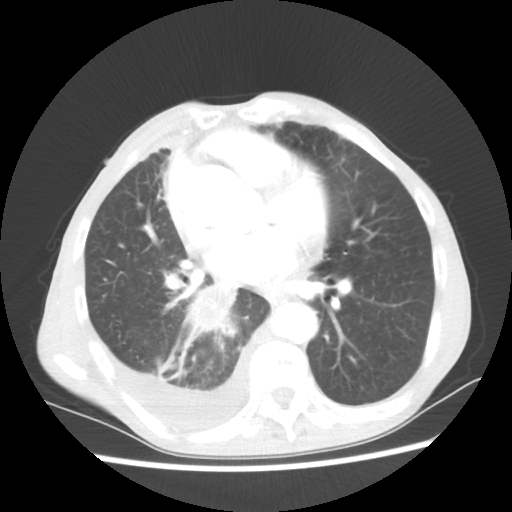
Chest CT, one axial slice; slice 27 of 60 in the series (ordered by position); lung window (W 1500 / L -600 HU); 5 mm slice thickness; 512 × 512 image matrix, field of view 335 × 335 mm. Patient: male, 76 years. From the clinical record (not read from this slice): clinical TNM (as recorded): T3 N3 M1a; histopathological grade: G3.
Annotated regions visible in this slice (rectangle marked by the reading radiologist):
- lung tumour (recorded histology: squamous cell carcinoma): box from (x=153, y=280) to (x=242, y=380) px